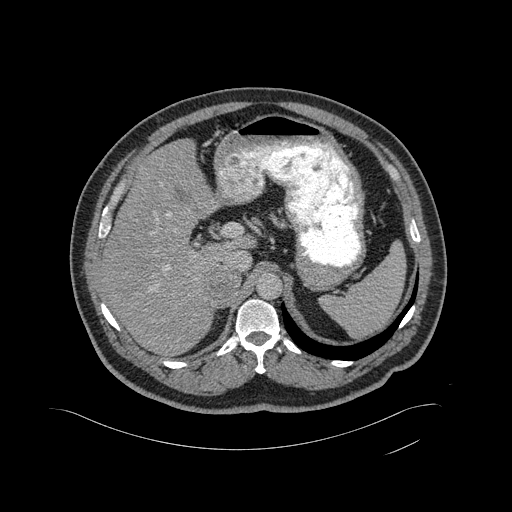
Contrast-enhanced abdominal CT, one axial slice; position 331 of 433 along the scan axis; intravenous contrast given; soft-tissue window (W 400 / L 40 HU); 2 mm slice thickness; 512 × 512 image matrix, field of view 500 × 500 mm. Patient: male, 56 years. From the clinical record (not read from this slice): diagnosis: adrenocortical carcinoma; tumour side: right adrenal; tumour size at pathology: 11.6 cm.
Structures marked on this image (semi-automatically segmented with operator editing):
- mass: box from (x=206, y=266) to (x=239, y=296) px